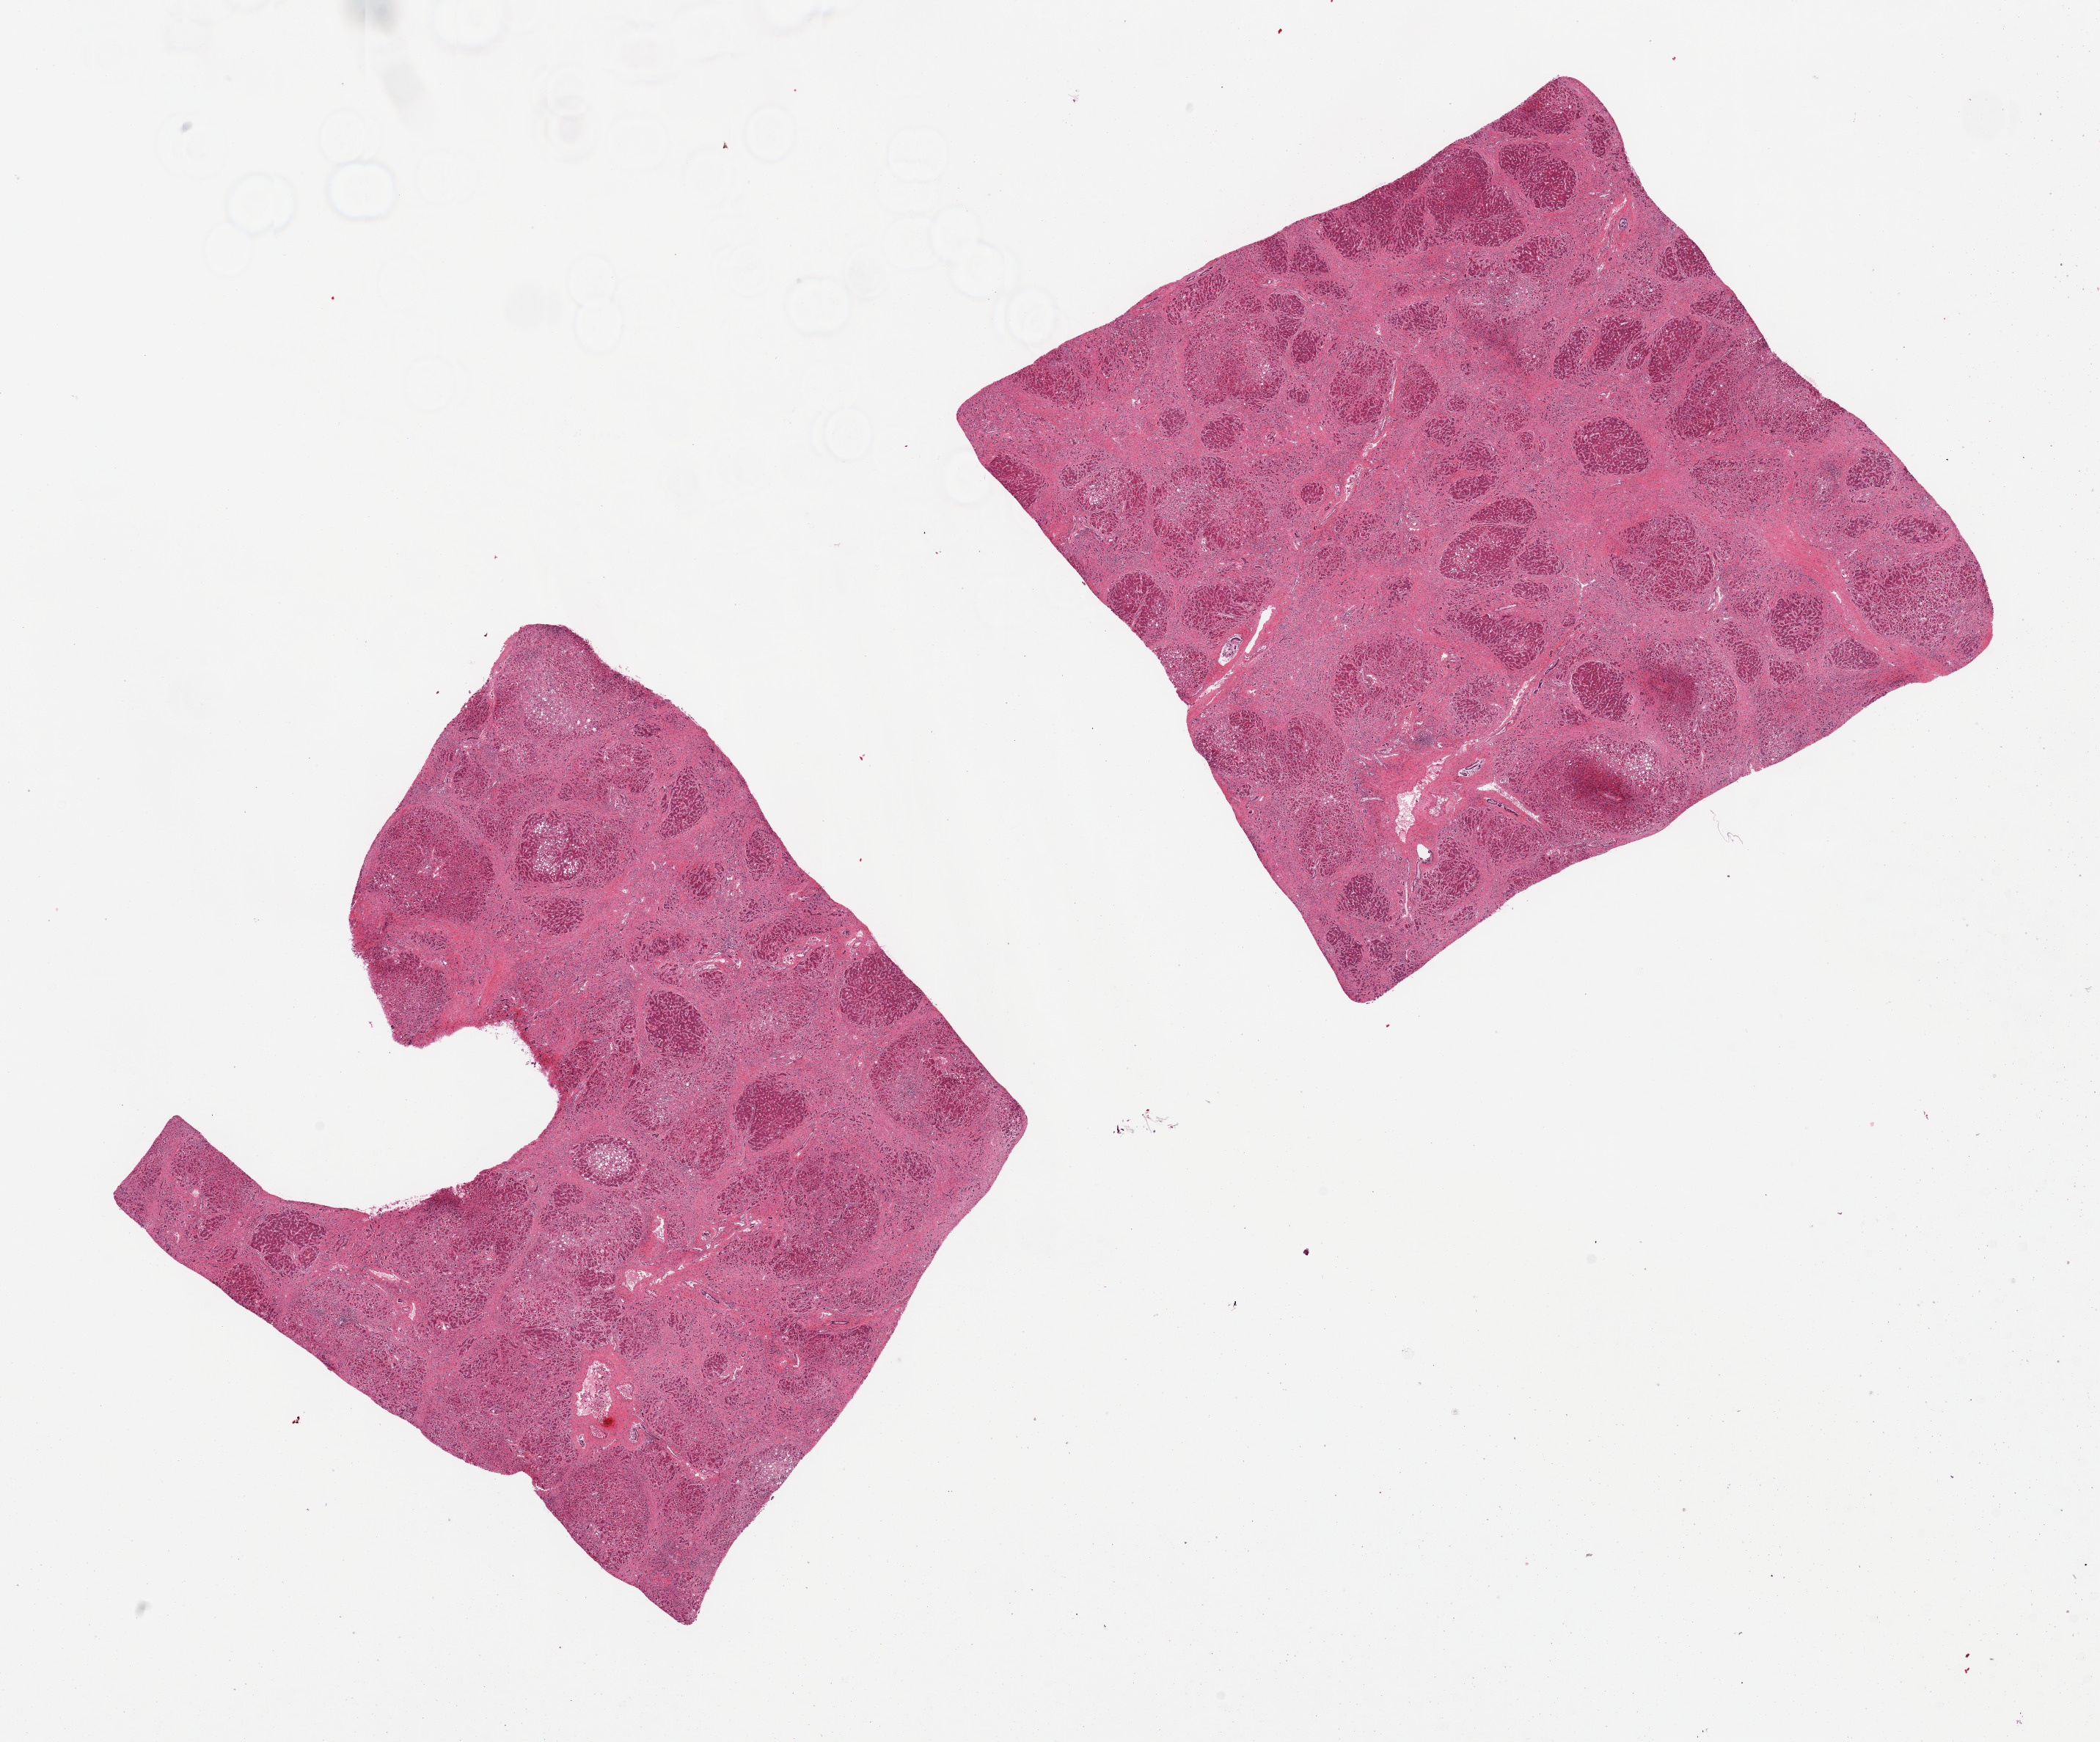
Hematoxylin and eosin (H&E) whole-slide image — whole scanned area (about 22.6 x 18.8 mm, acquisition: 20x scan) shown as a low-resolution overview, PAXgene-fixed paraffin-embedded (PFPE) section, sampled site (target tissue): liver, tissue donor sample. Donor: male.
- reviewer comment on this tissue sample: 2 pieces; severe cirrhosis, some residual chronic inflammation and steatosis